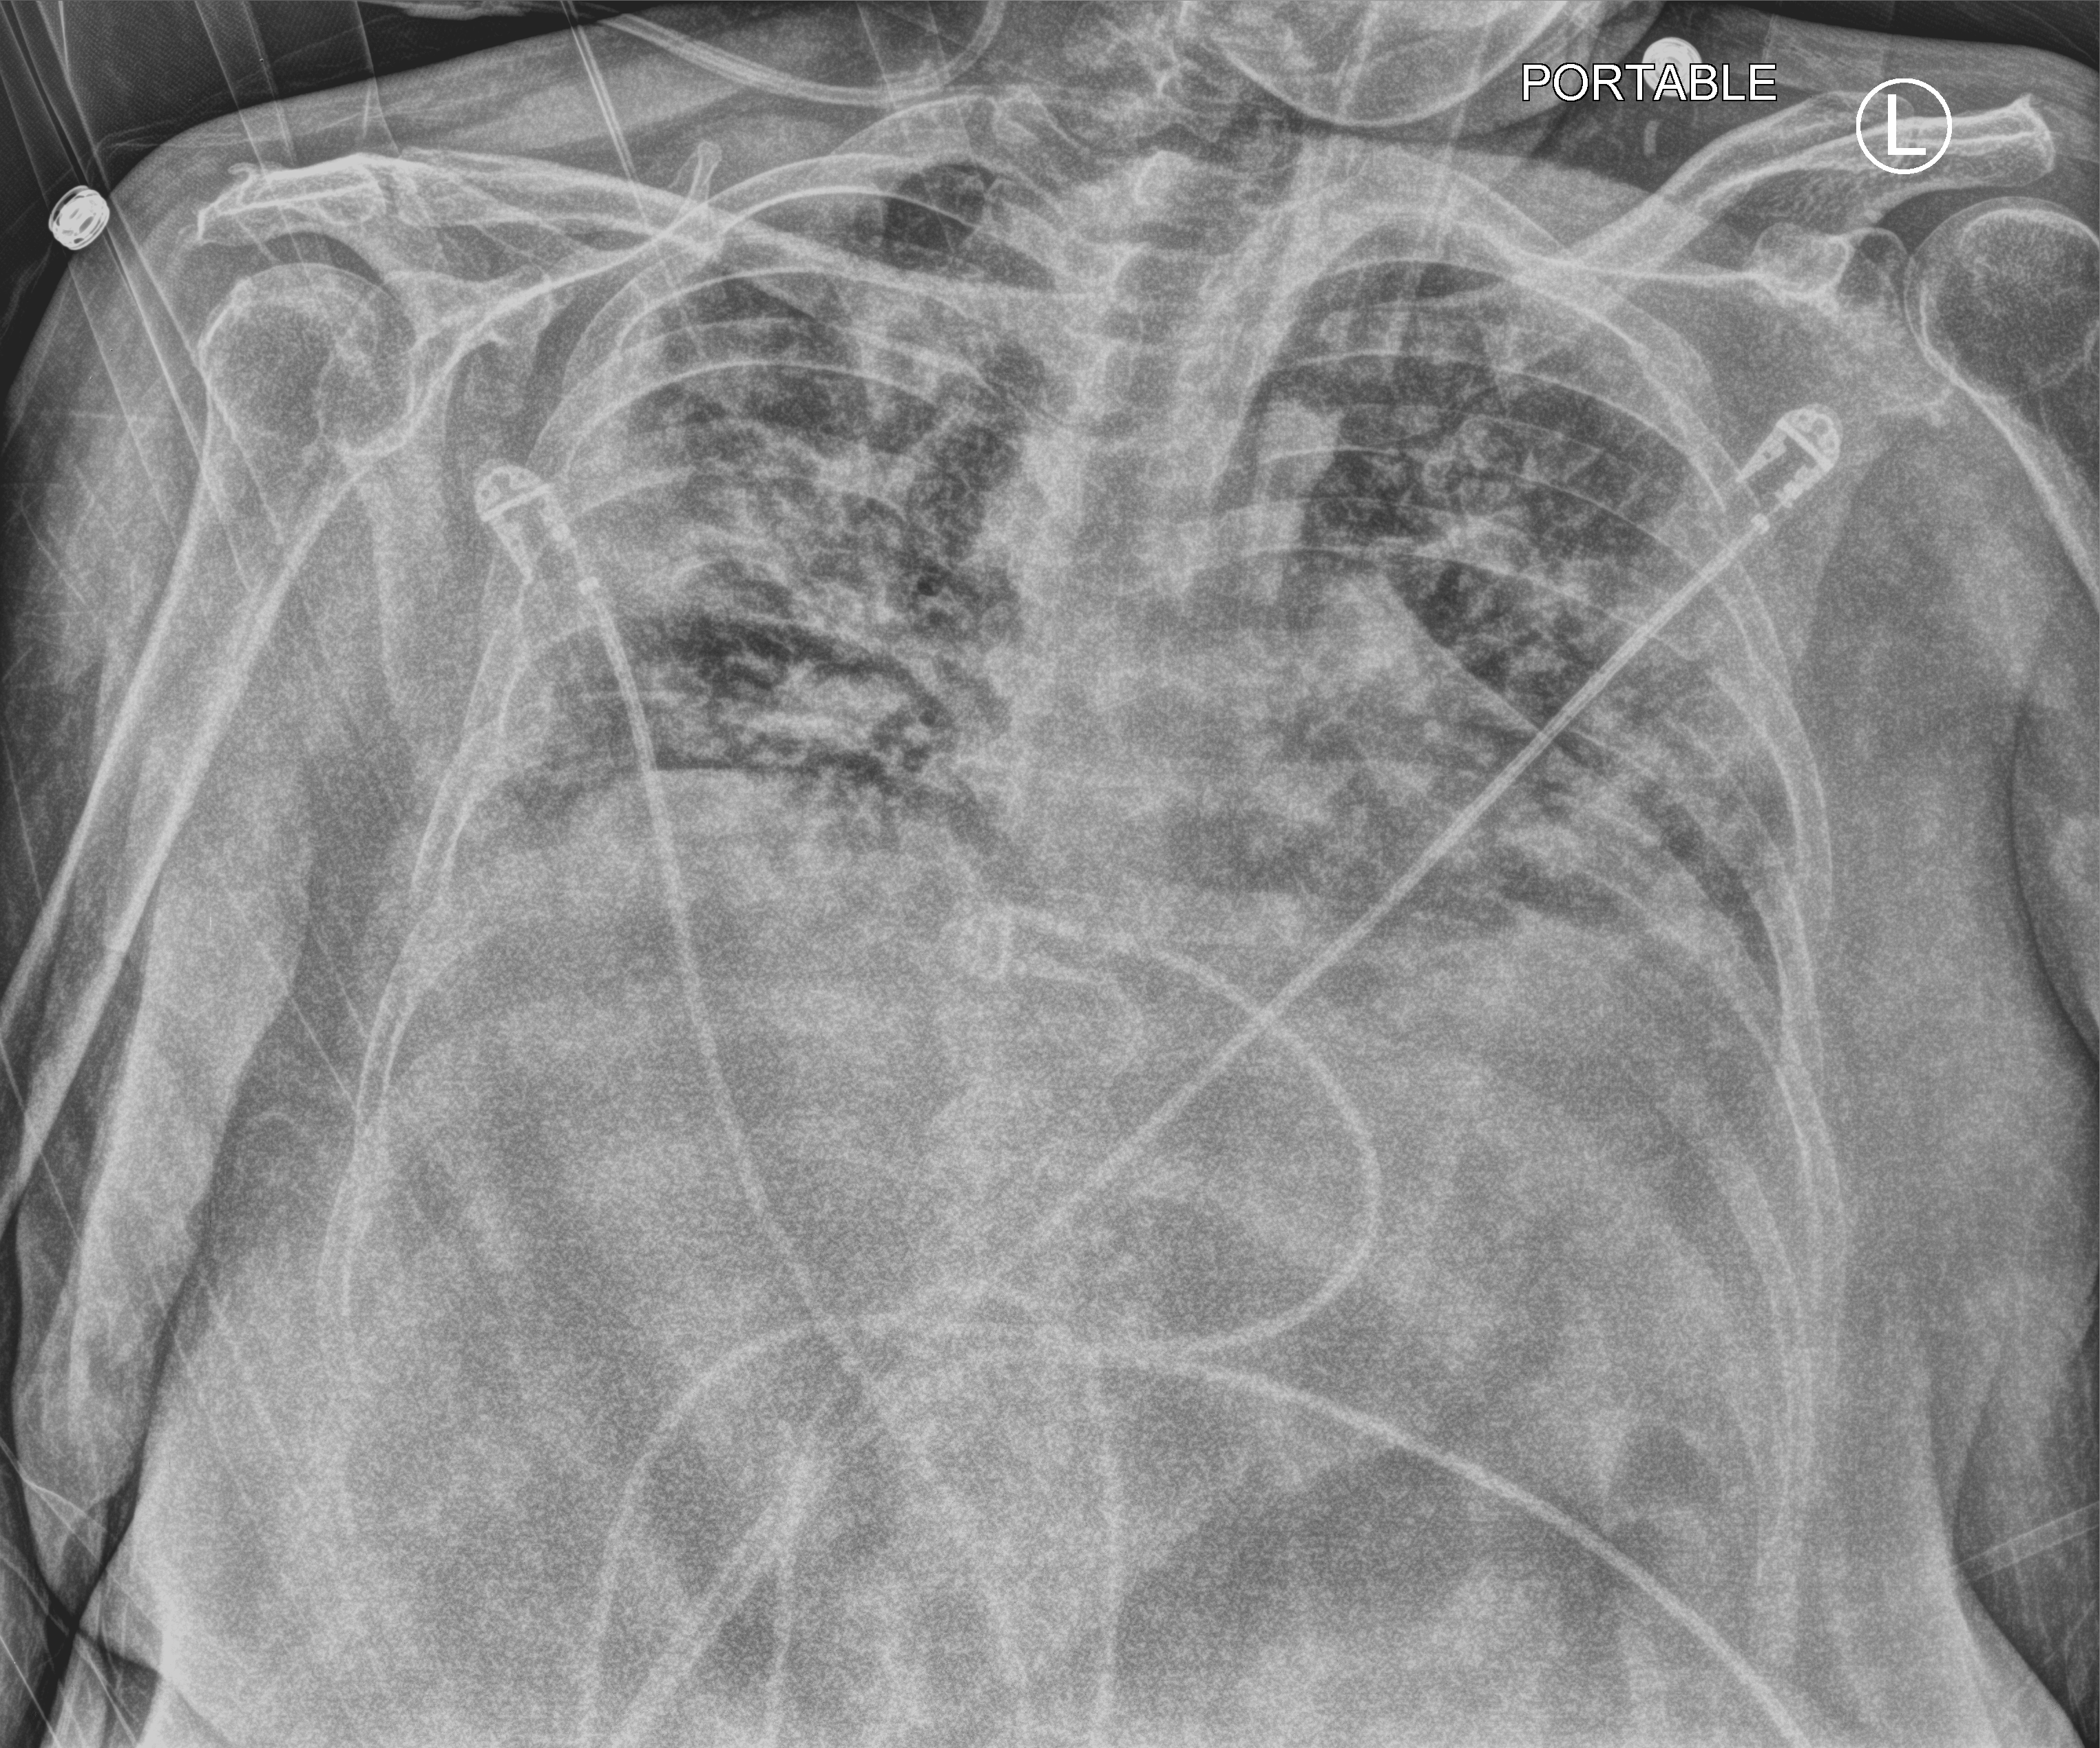
Chest X-ray (portable), anteroposterior (AP) projection. Patient hospitalised with COVID-19; female, aged 18–59 years.
From the hospital-stay record, not from the radiograph (when in the stay this image was taken is not recorded):
- admitted to intensive care during this hospital stay: yes
- mechanically ventilated during this hospital stay: no